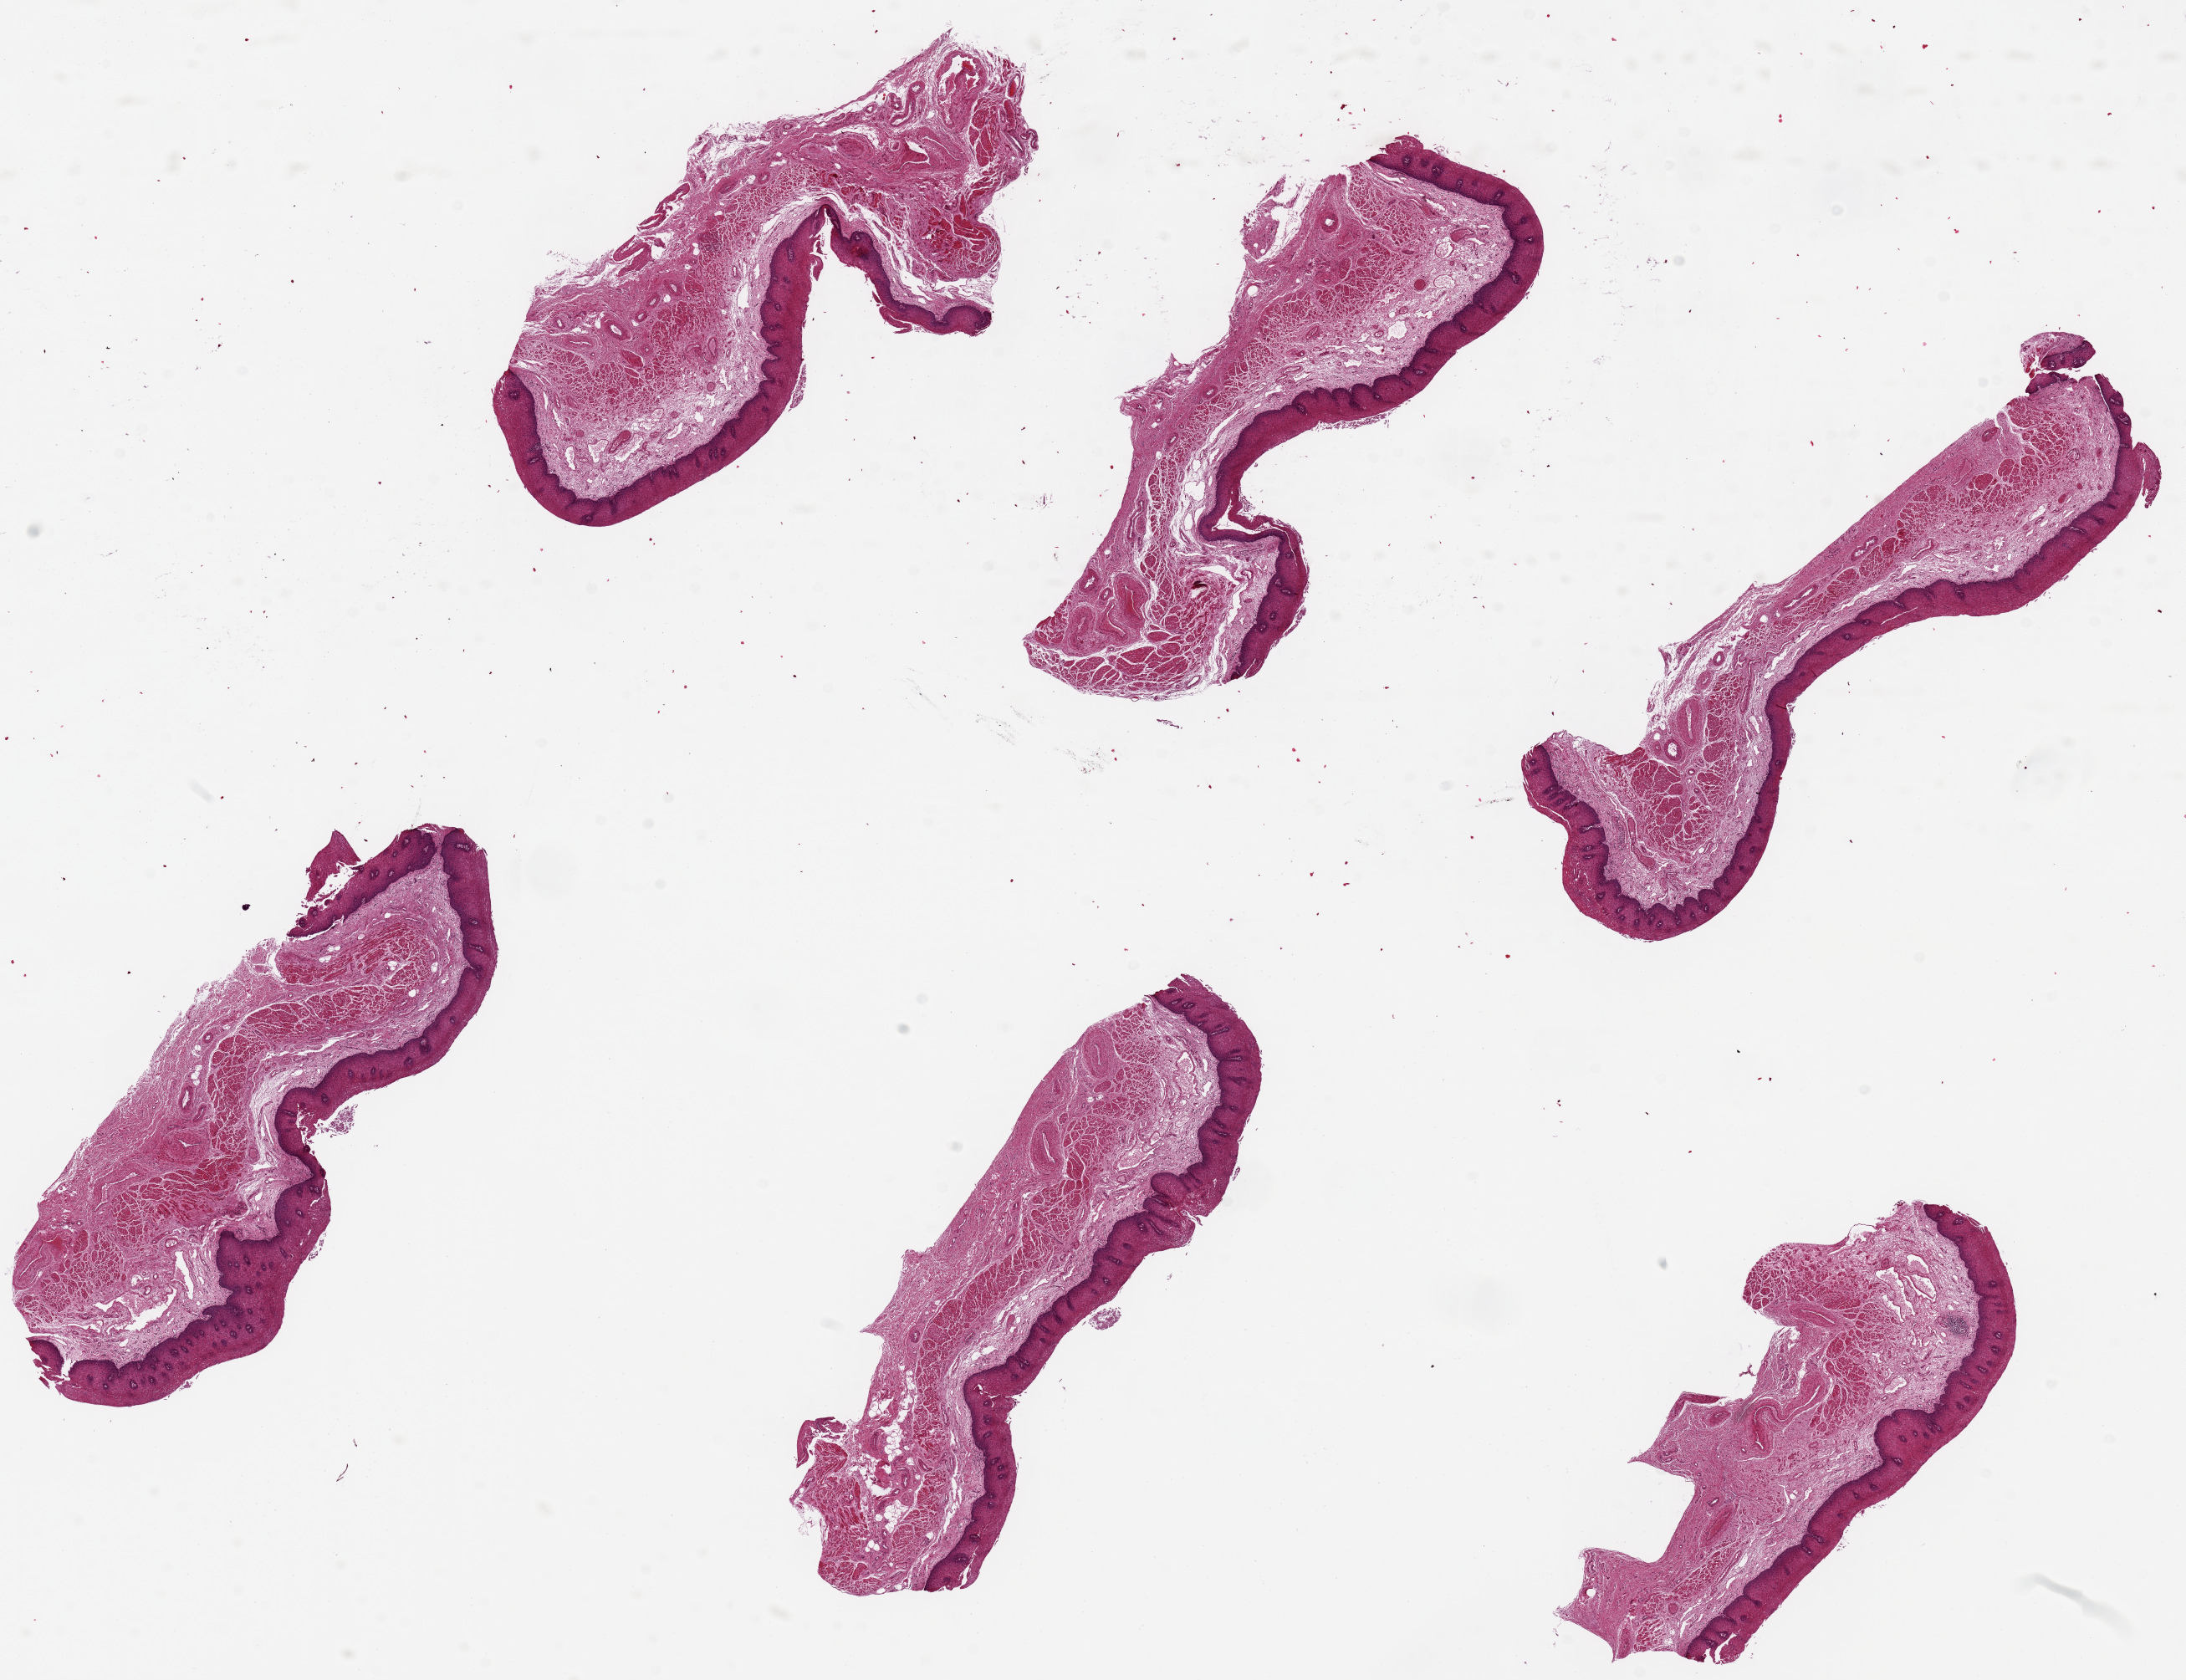
Haematoxylin and eosin whole-slide image, brightfield, shown as a low-resolution overview of the whole scanned area (about 20.7 x 15.9 mm, slide scanned at 20x); PAXgene-fixed paraffin-embedded (PFPE) section; sampled site (target tissue): esophageal mucous membrane; donor tissue sample. Male donor.
* pathologist's review note for this sample: 6 pieces ~6x2mm, squamous mucosa is ~10-15% thickness